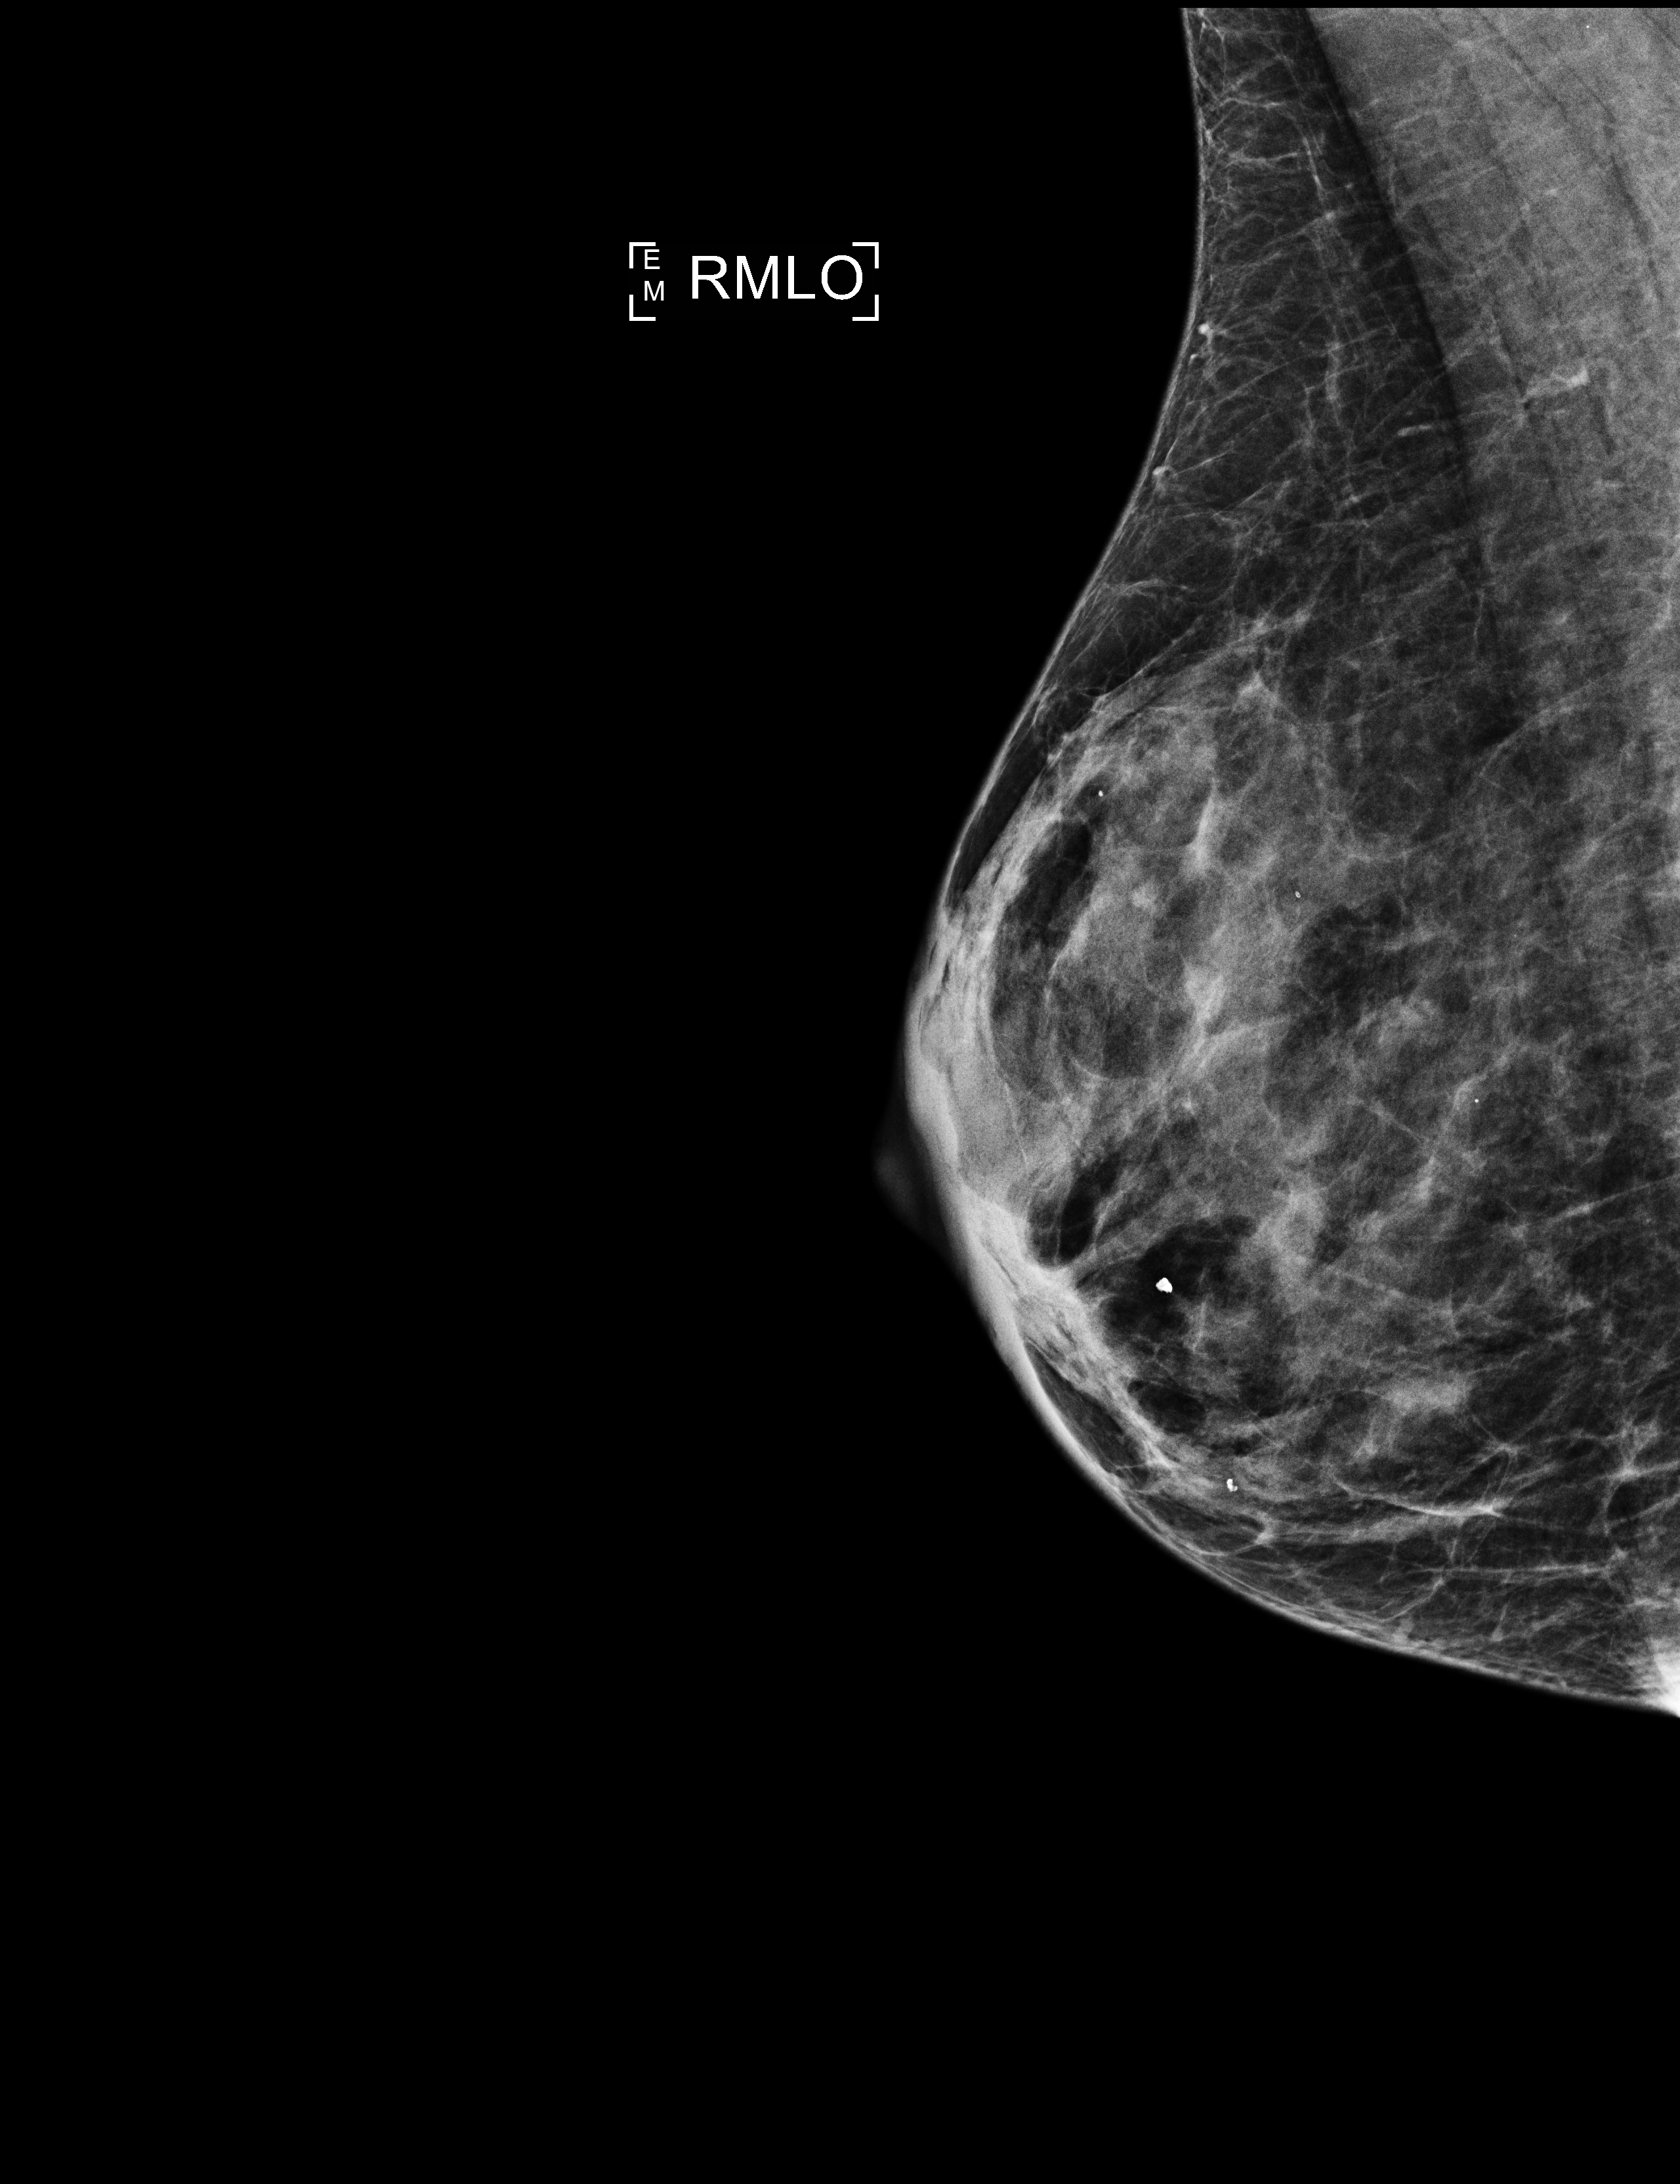
Digital mammogram (FFDM), right breast, MLO view, screening examination, compressed breast thickness 33 mm. Patient: female, 65 years.
Breast density at the screening exam (both breasts): extremely dense (BI-RADS density category d). Final BI-RADS category for the screening round (tomosynthesis exam, both breasts): category 2. Recall: recalled for additional imaging after this screen.